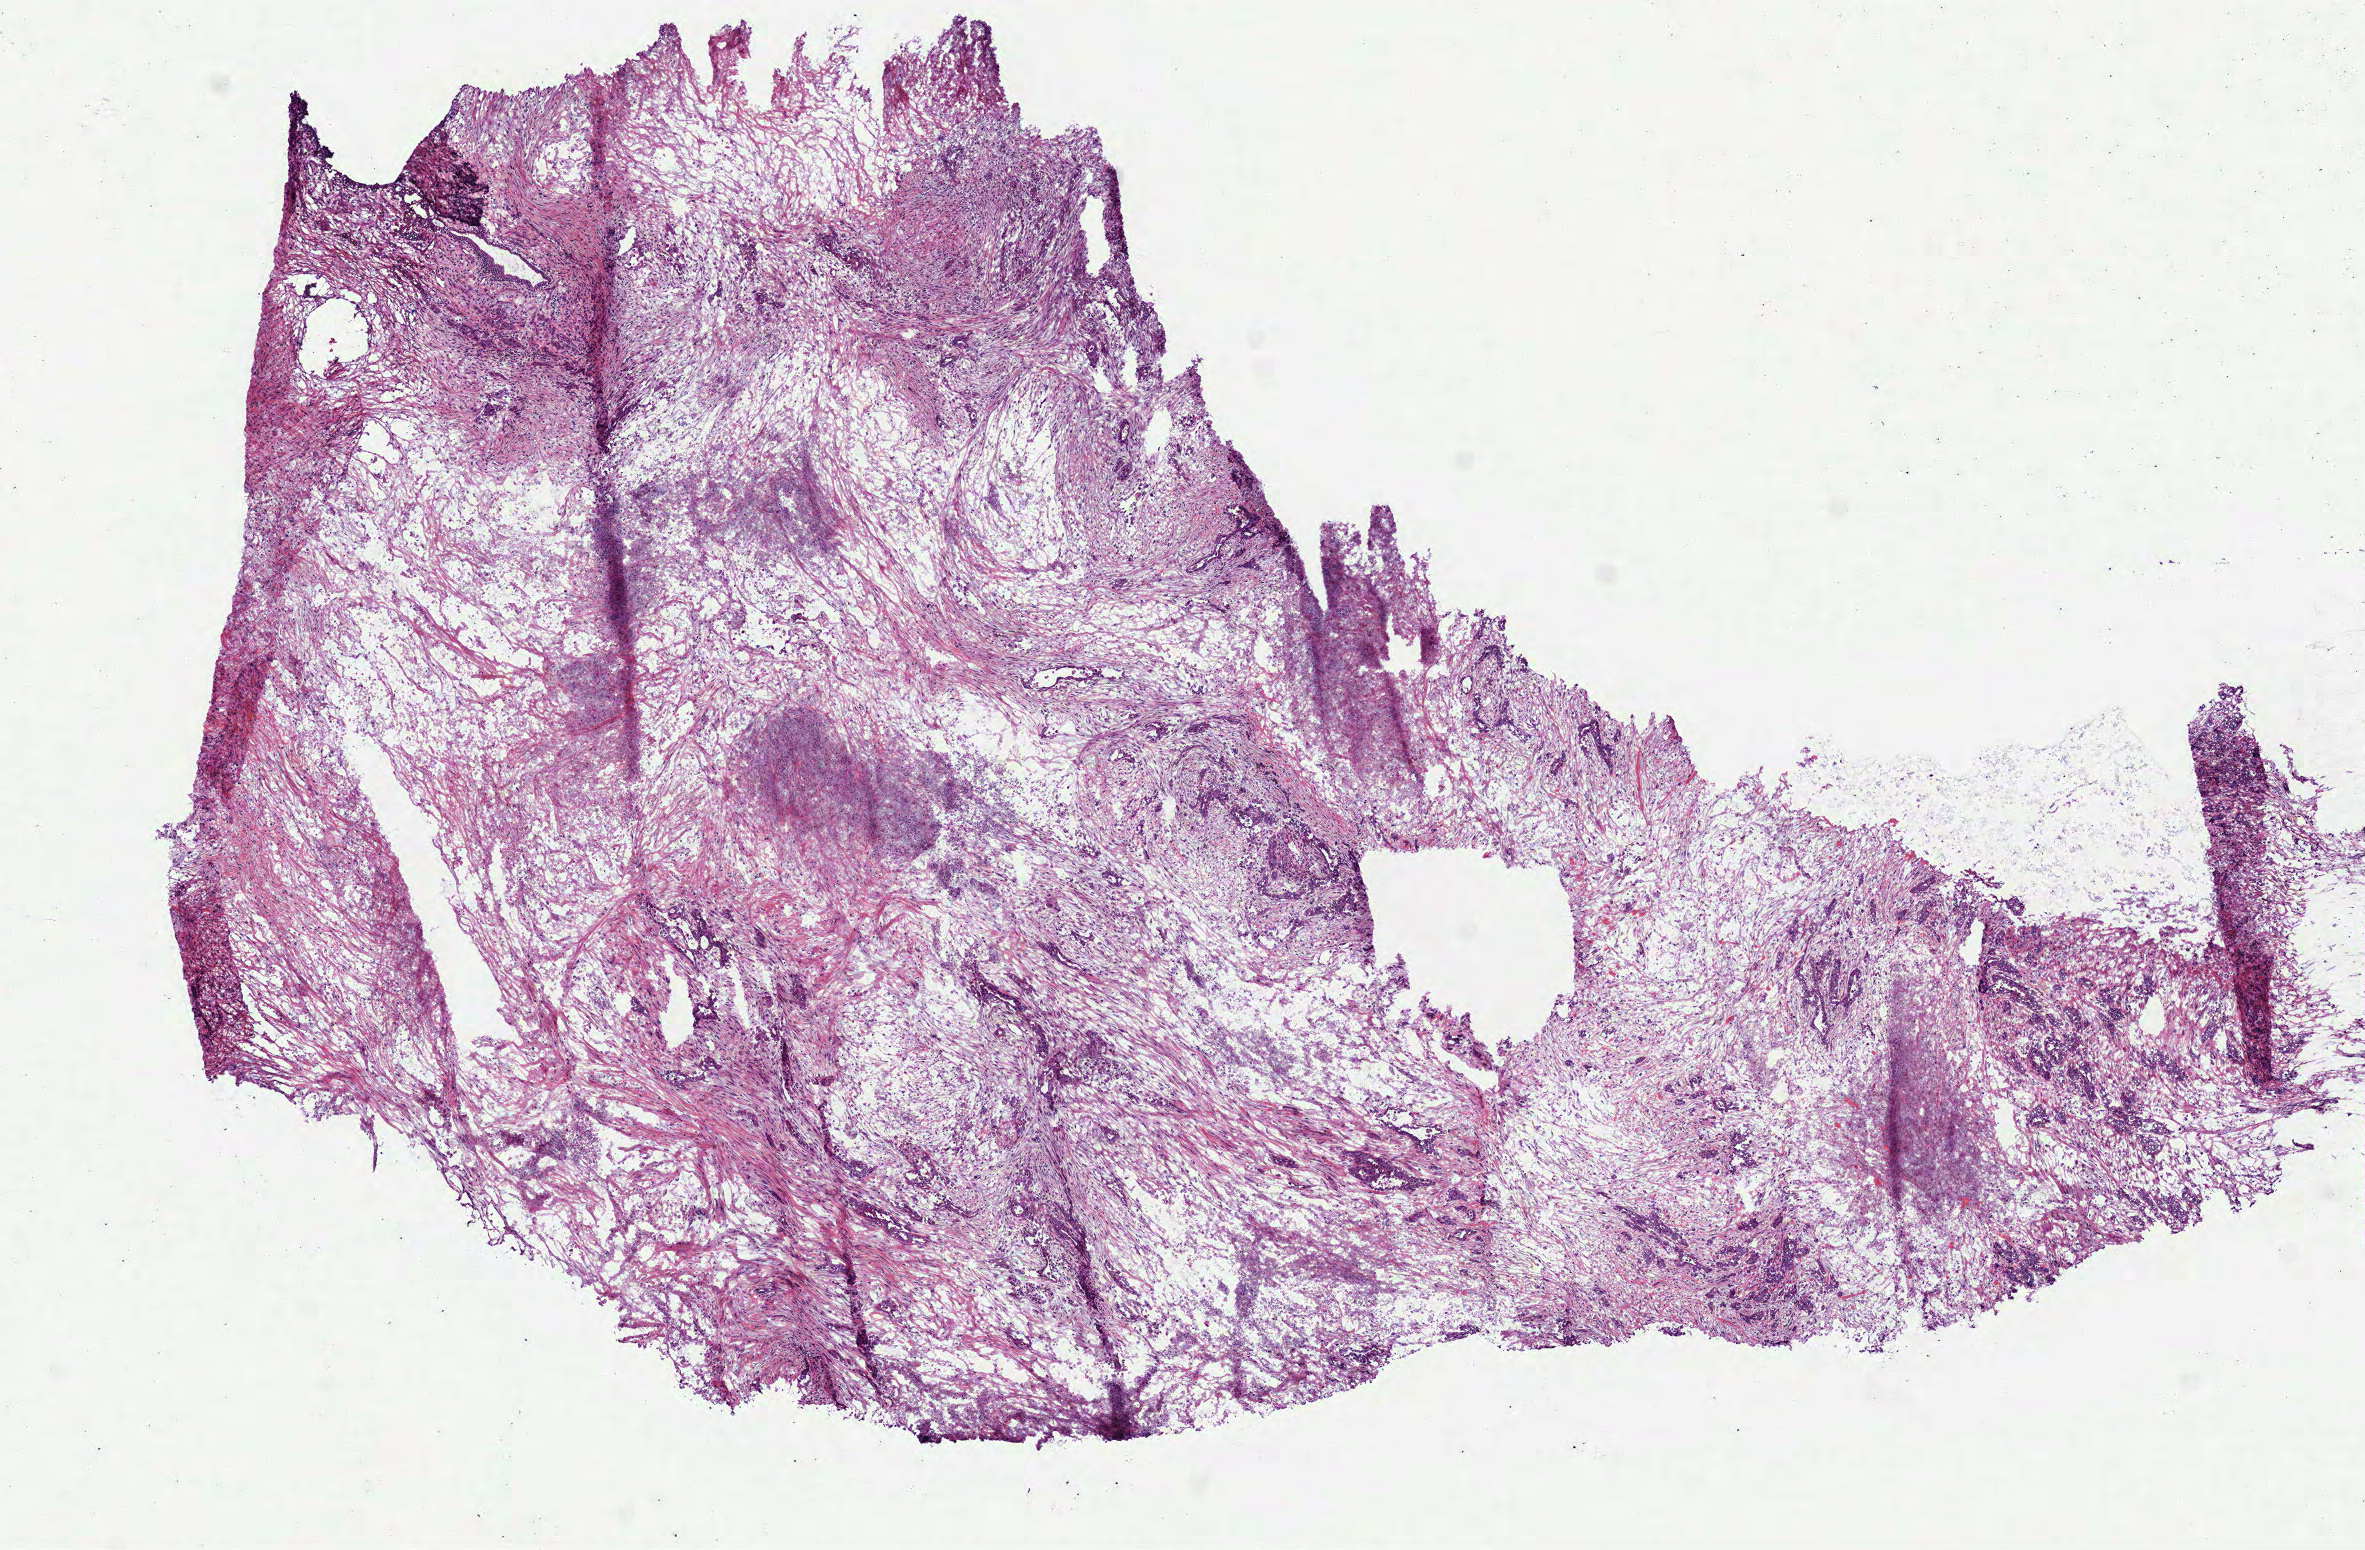
Hematoxylin and eosin (H&E) stained whole-slide image — low-resolution overview of the scanned area, about 9.5 x 6.3 mm. Frozen section from the bottom of the tissue portion. Primary tumour sample from the pancreas. Male, age 81 years at initial diagnosis. Histologic grade: G3 (poorly differentiated).
- lymph nodes positive (case pathology): 8 of 24 examined
- pathologic diagnosis: Infiltrating duct carcinoma, NOS
- AJCC pathologic stage: IIB